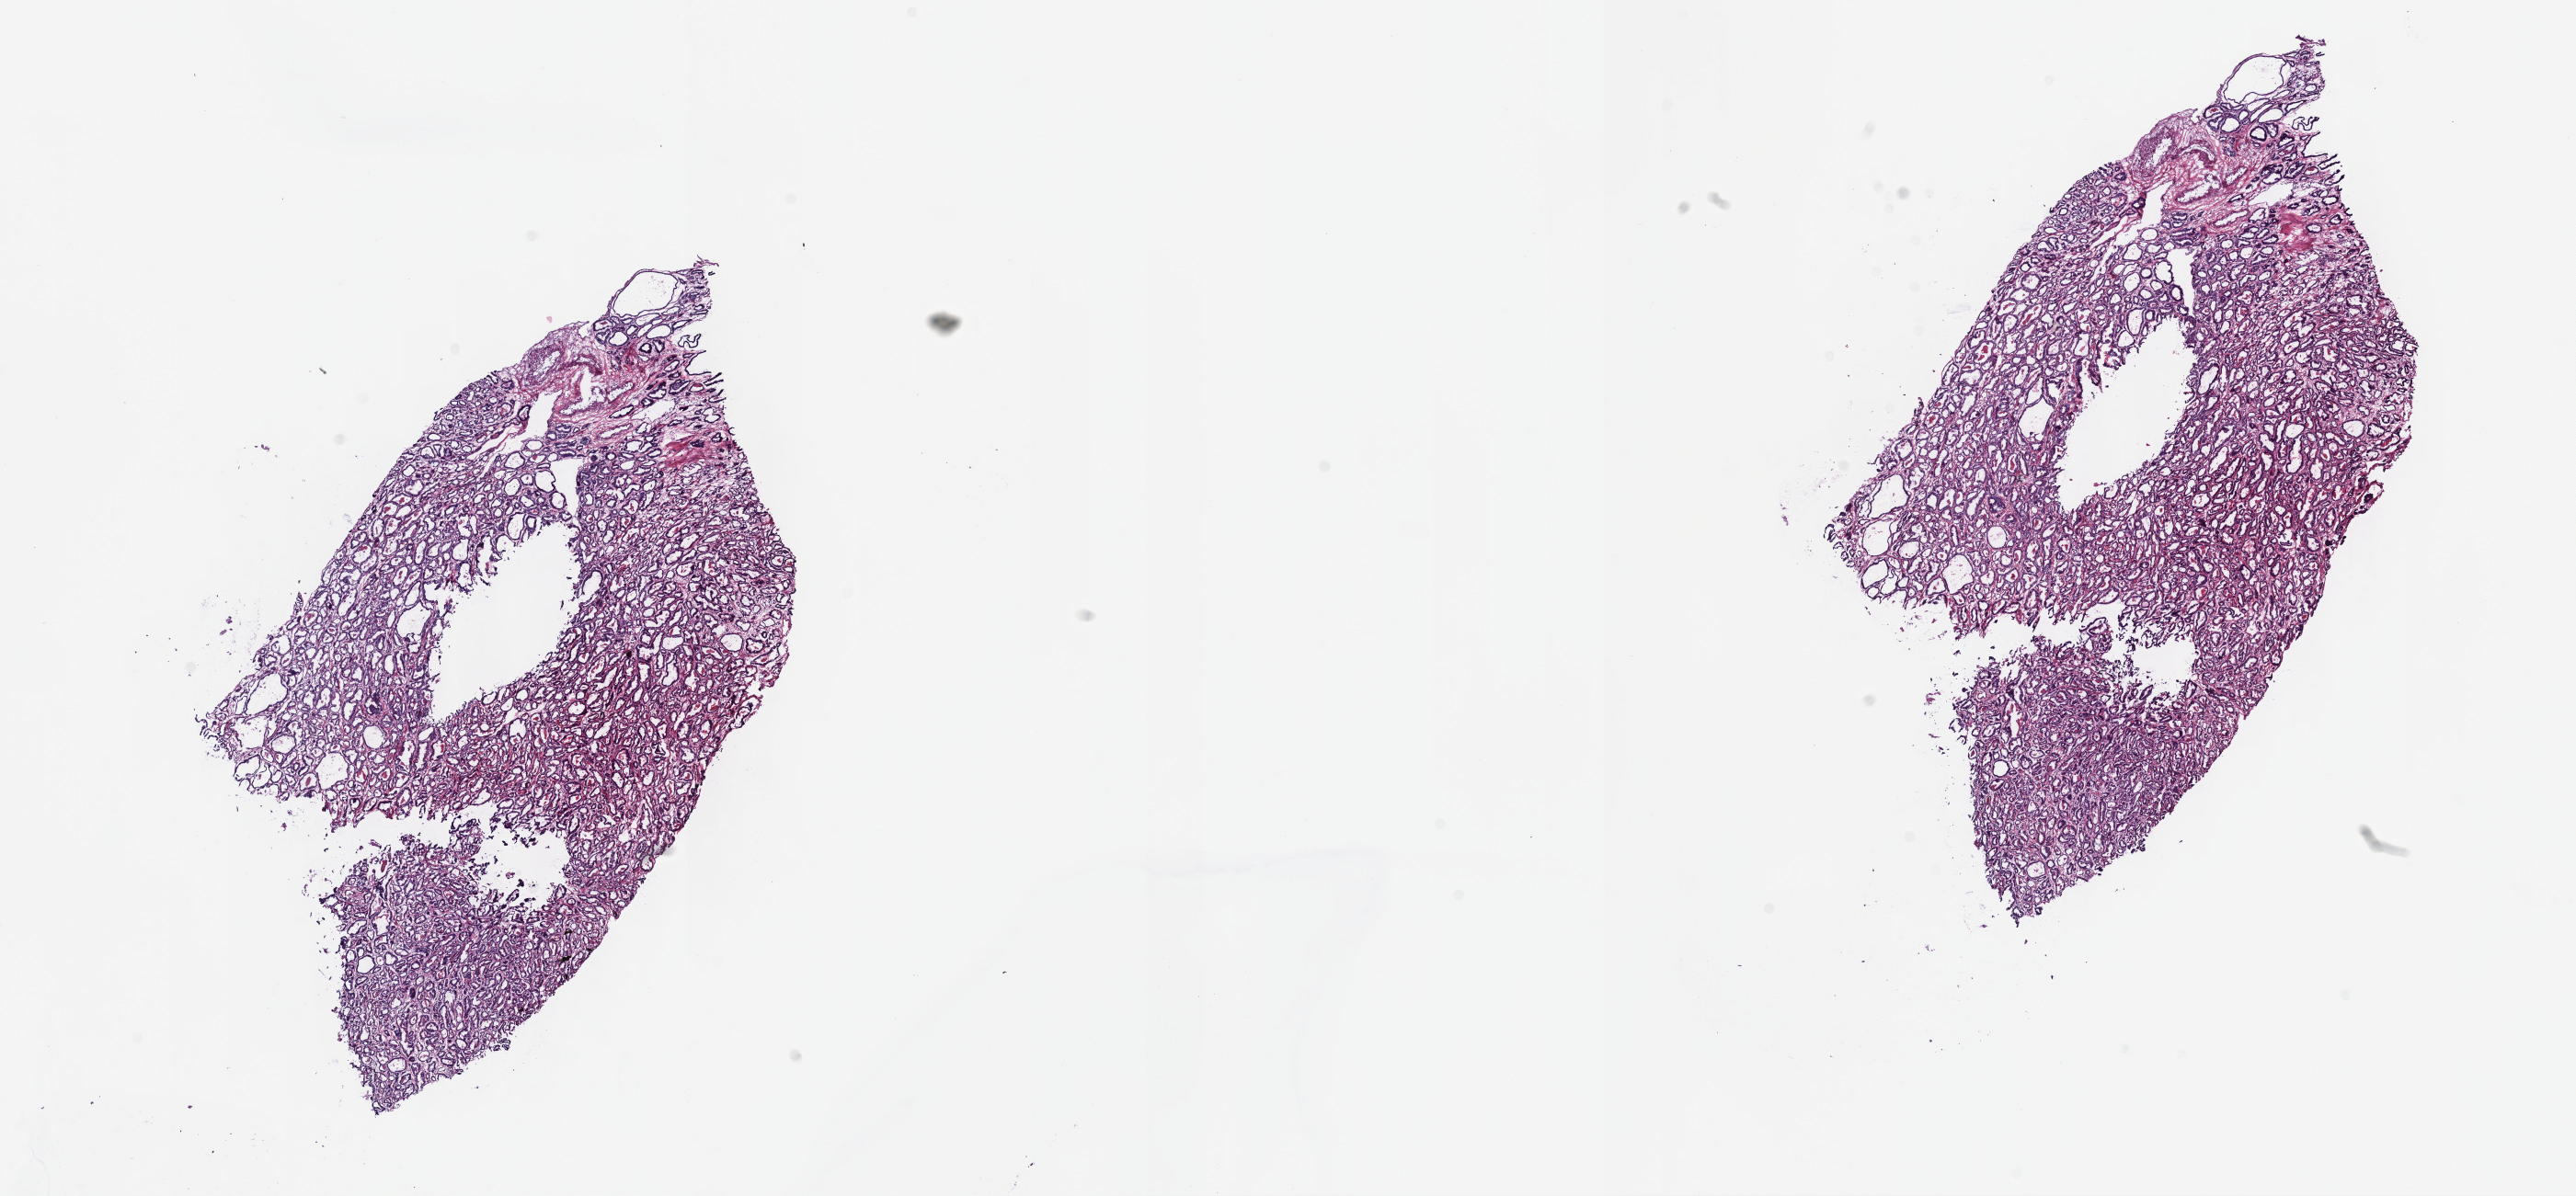
Digitized Hematoxylin and eosin (H&E) stained tissue section (whole slide) — whole scanned area (about 22.7 x 10.5 mm, acquisition: 40x scan) shown as a low-resolution overview, frozen section from the top of the tissue portion, primary tumour sample from the prostate. Male, age 71 years at initial diagnosis. Gleason score: 8 (4+4). Composition of this section per pathologist review: tumour cells 95%, tumour nuclei 77%, normal cells 5%, stromal cells 0%, necrosis 0%. Inflammatory infiltration, as recorded: lymphocyte infiltration 0%, monocyte infiltration 0%, neutrophil infiltration 0%.
* diagnosis: Adenocarcinoma, NOS (prostate gland)
* lymph nodes positive (case pathology): 0 of 10 examined